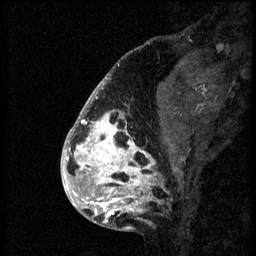
Breast MRI (dynamic contrast-enhanced), one sagittal slice; position 21 of 60 along the scan axis; 3 images stored at this slice position (order not interpretable as contrast timing); 1.5 T; TE 4.2 ms, TR 8.2 ms; 2 mm slice thickness; 256 × 256 image matrix, field of view 180 × 180 mm. Patient: female, 41 years.
Outlined on this slice (semi-automatically segmented with operator editing):
- analysis volume of interest (the breast-tissue region the enhancement analysis was run in; not a lesion): bounding box <72,108,176,205> (left, top, right, bottom; pixels)
- tumour enhancement mask (voxels above the 70 % enhancement threshold inside the analysis volume of interest): <72,108,164,205>